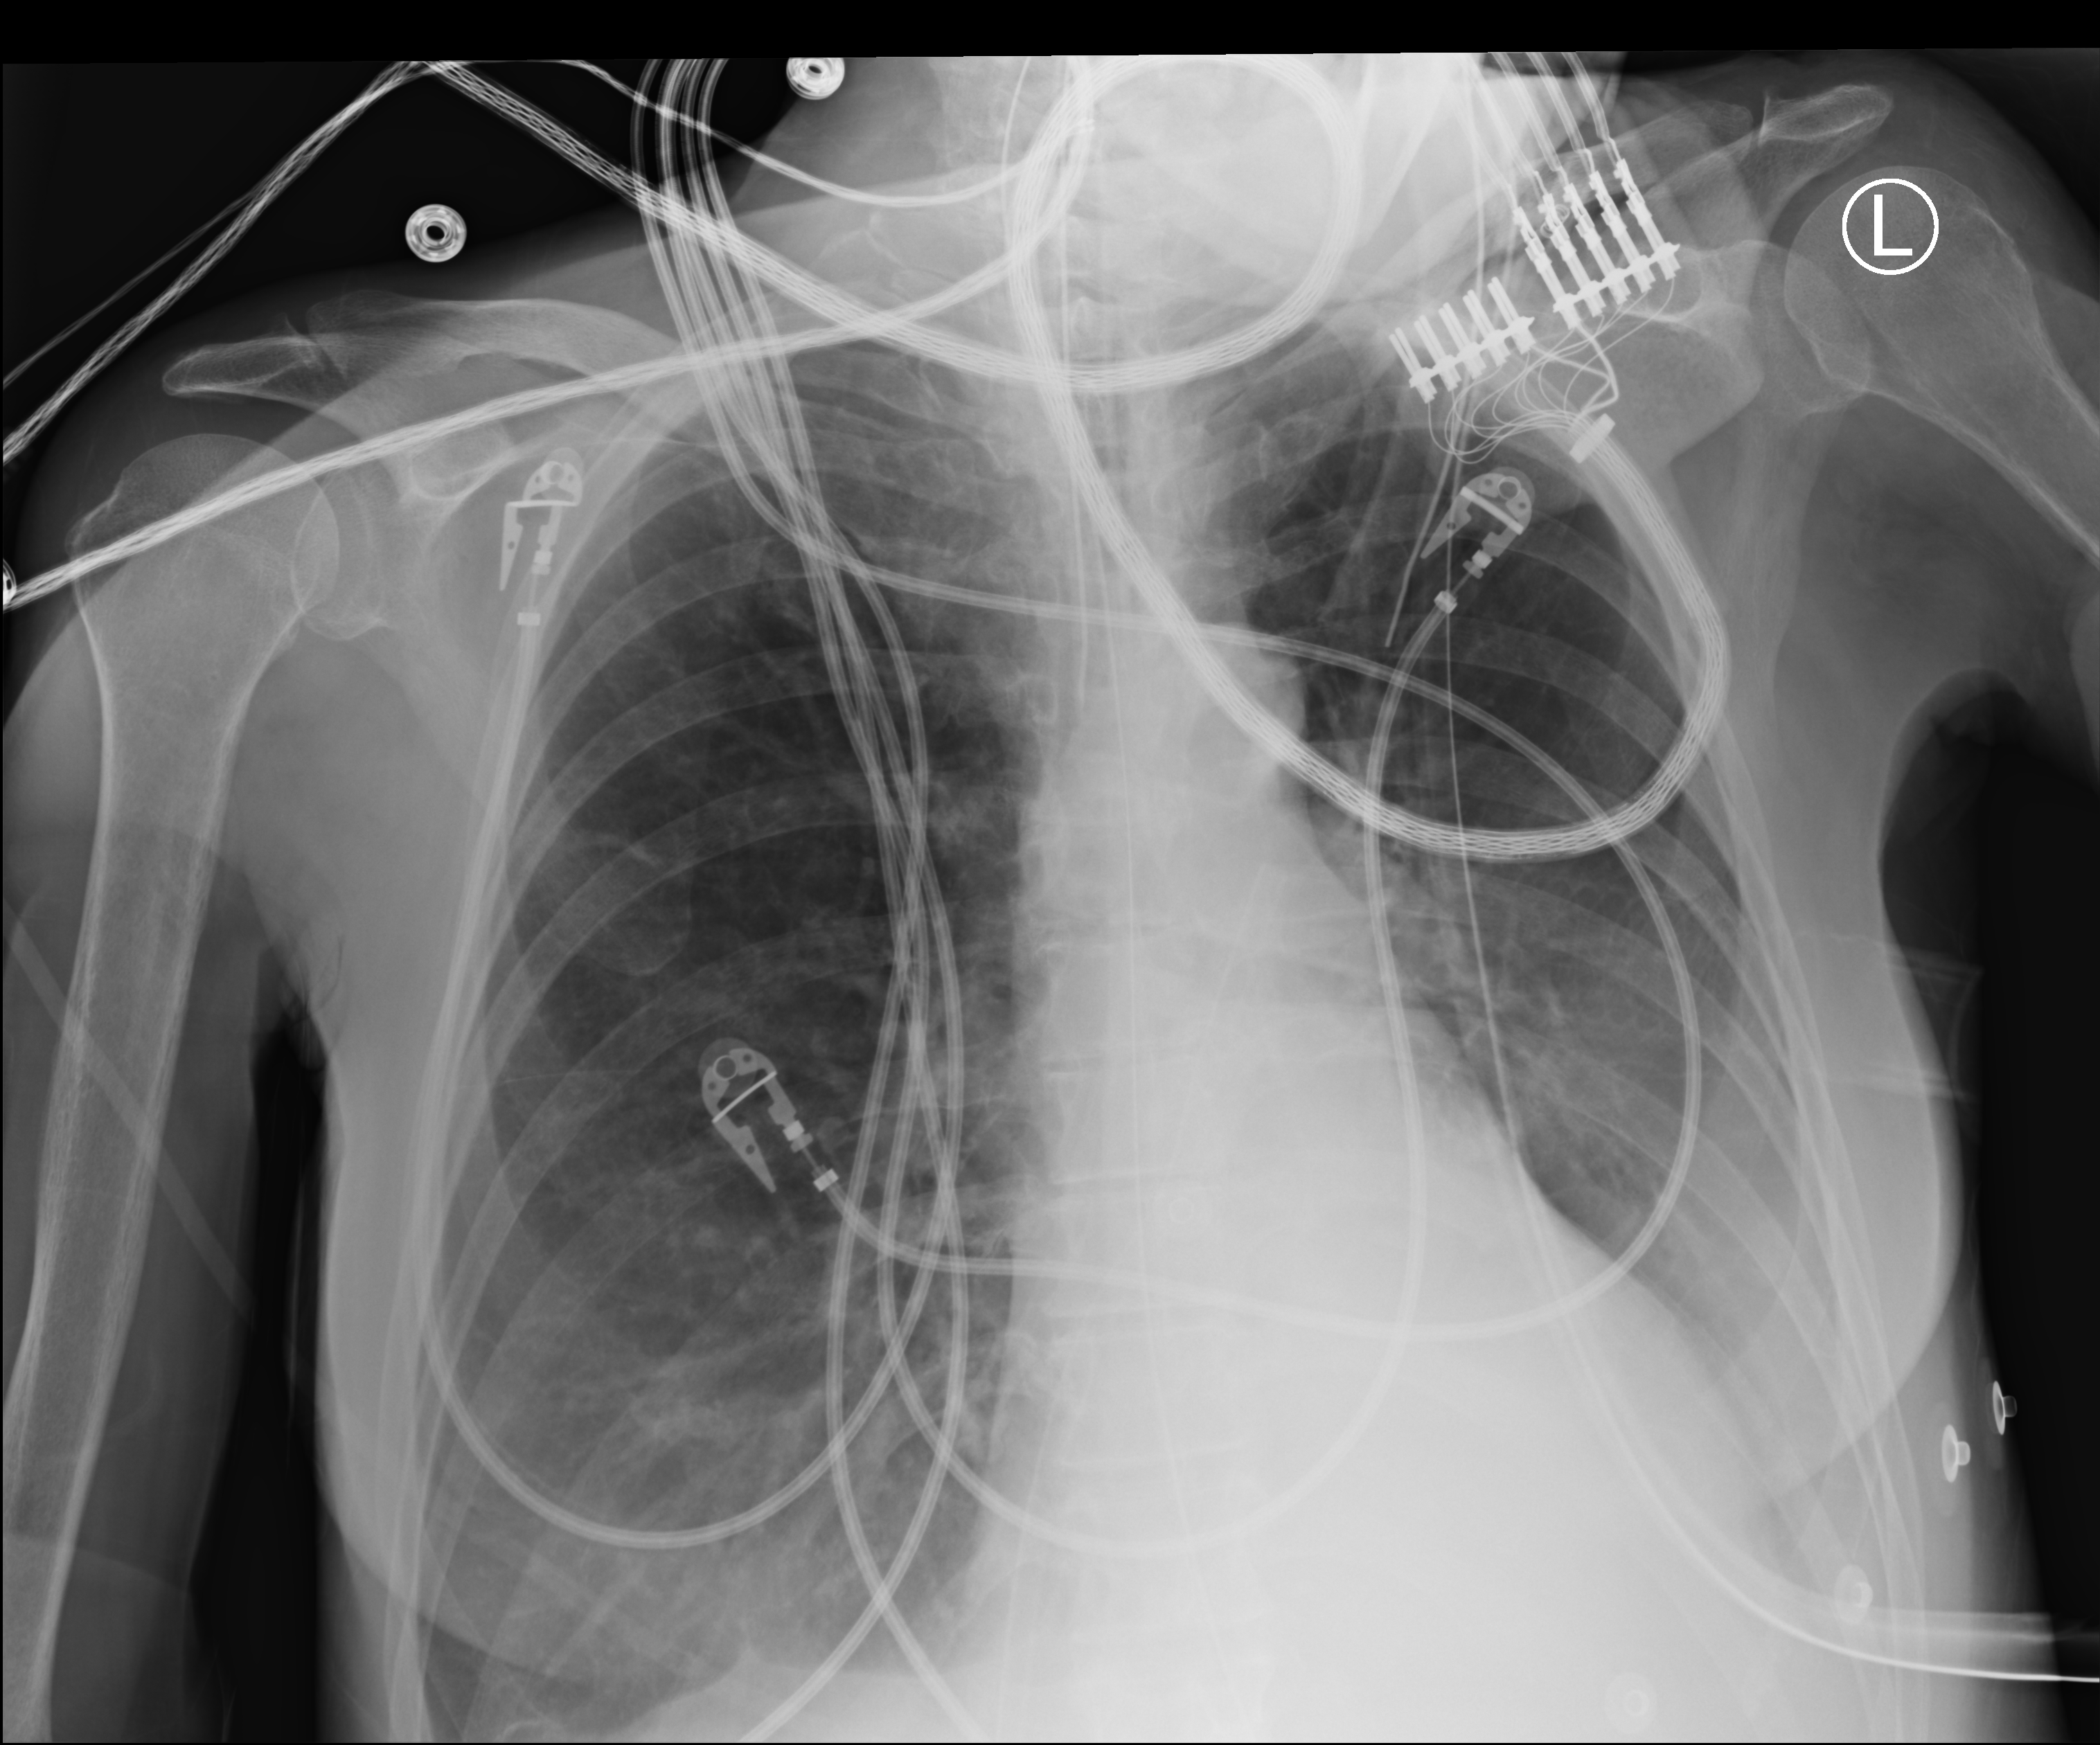
Portable chest radiograph, anteroposterior (AP) projection. Patient hospitalised with COVID-19; female, aged 60–74 years.
Hospital-stay facts (about this admission, not read from this image; timing relative to this image not recorded): admitted to intensive care during this hospital stay: yes.